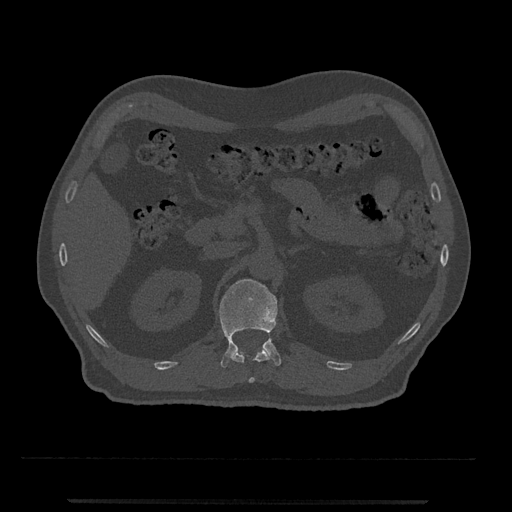
CT including the spine, one axial slice; slice 363 of 797 in the series (ordered by position); 120 kVp; bone window (W 1800 / L 400 HU); 512 × 512 image matrix. Patient: male, 63 years. From the clinical record (not read from this slice): primary cancer: prostate.
Structures marked on this image (semi-automatic segmentation, software-assisted and operator-edited):
- L1 vertebra: bounding box (x1, y1, x2, y2) in pixels: (219, 279, 281, 368)
- T12 vertebra: (231, 348, 271, 383)